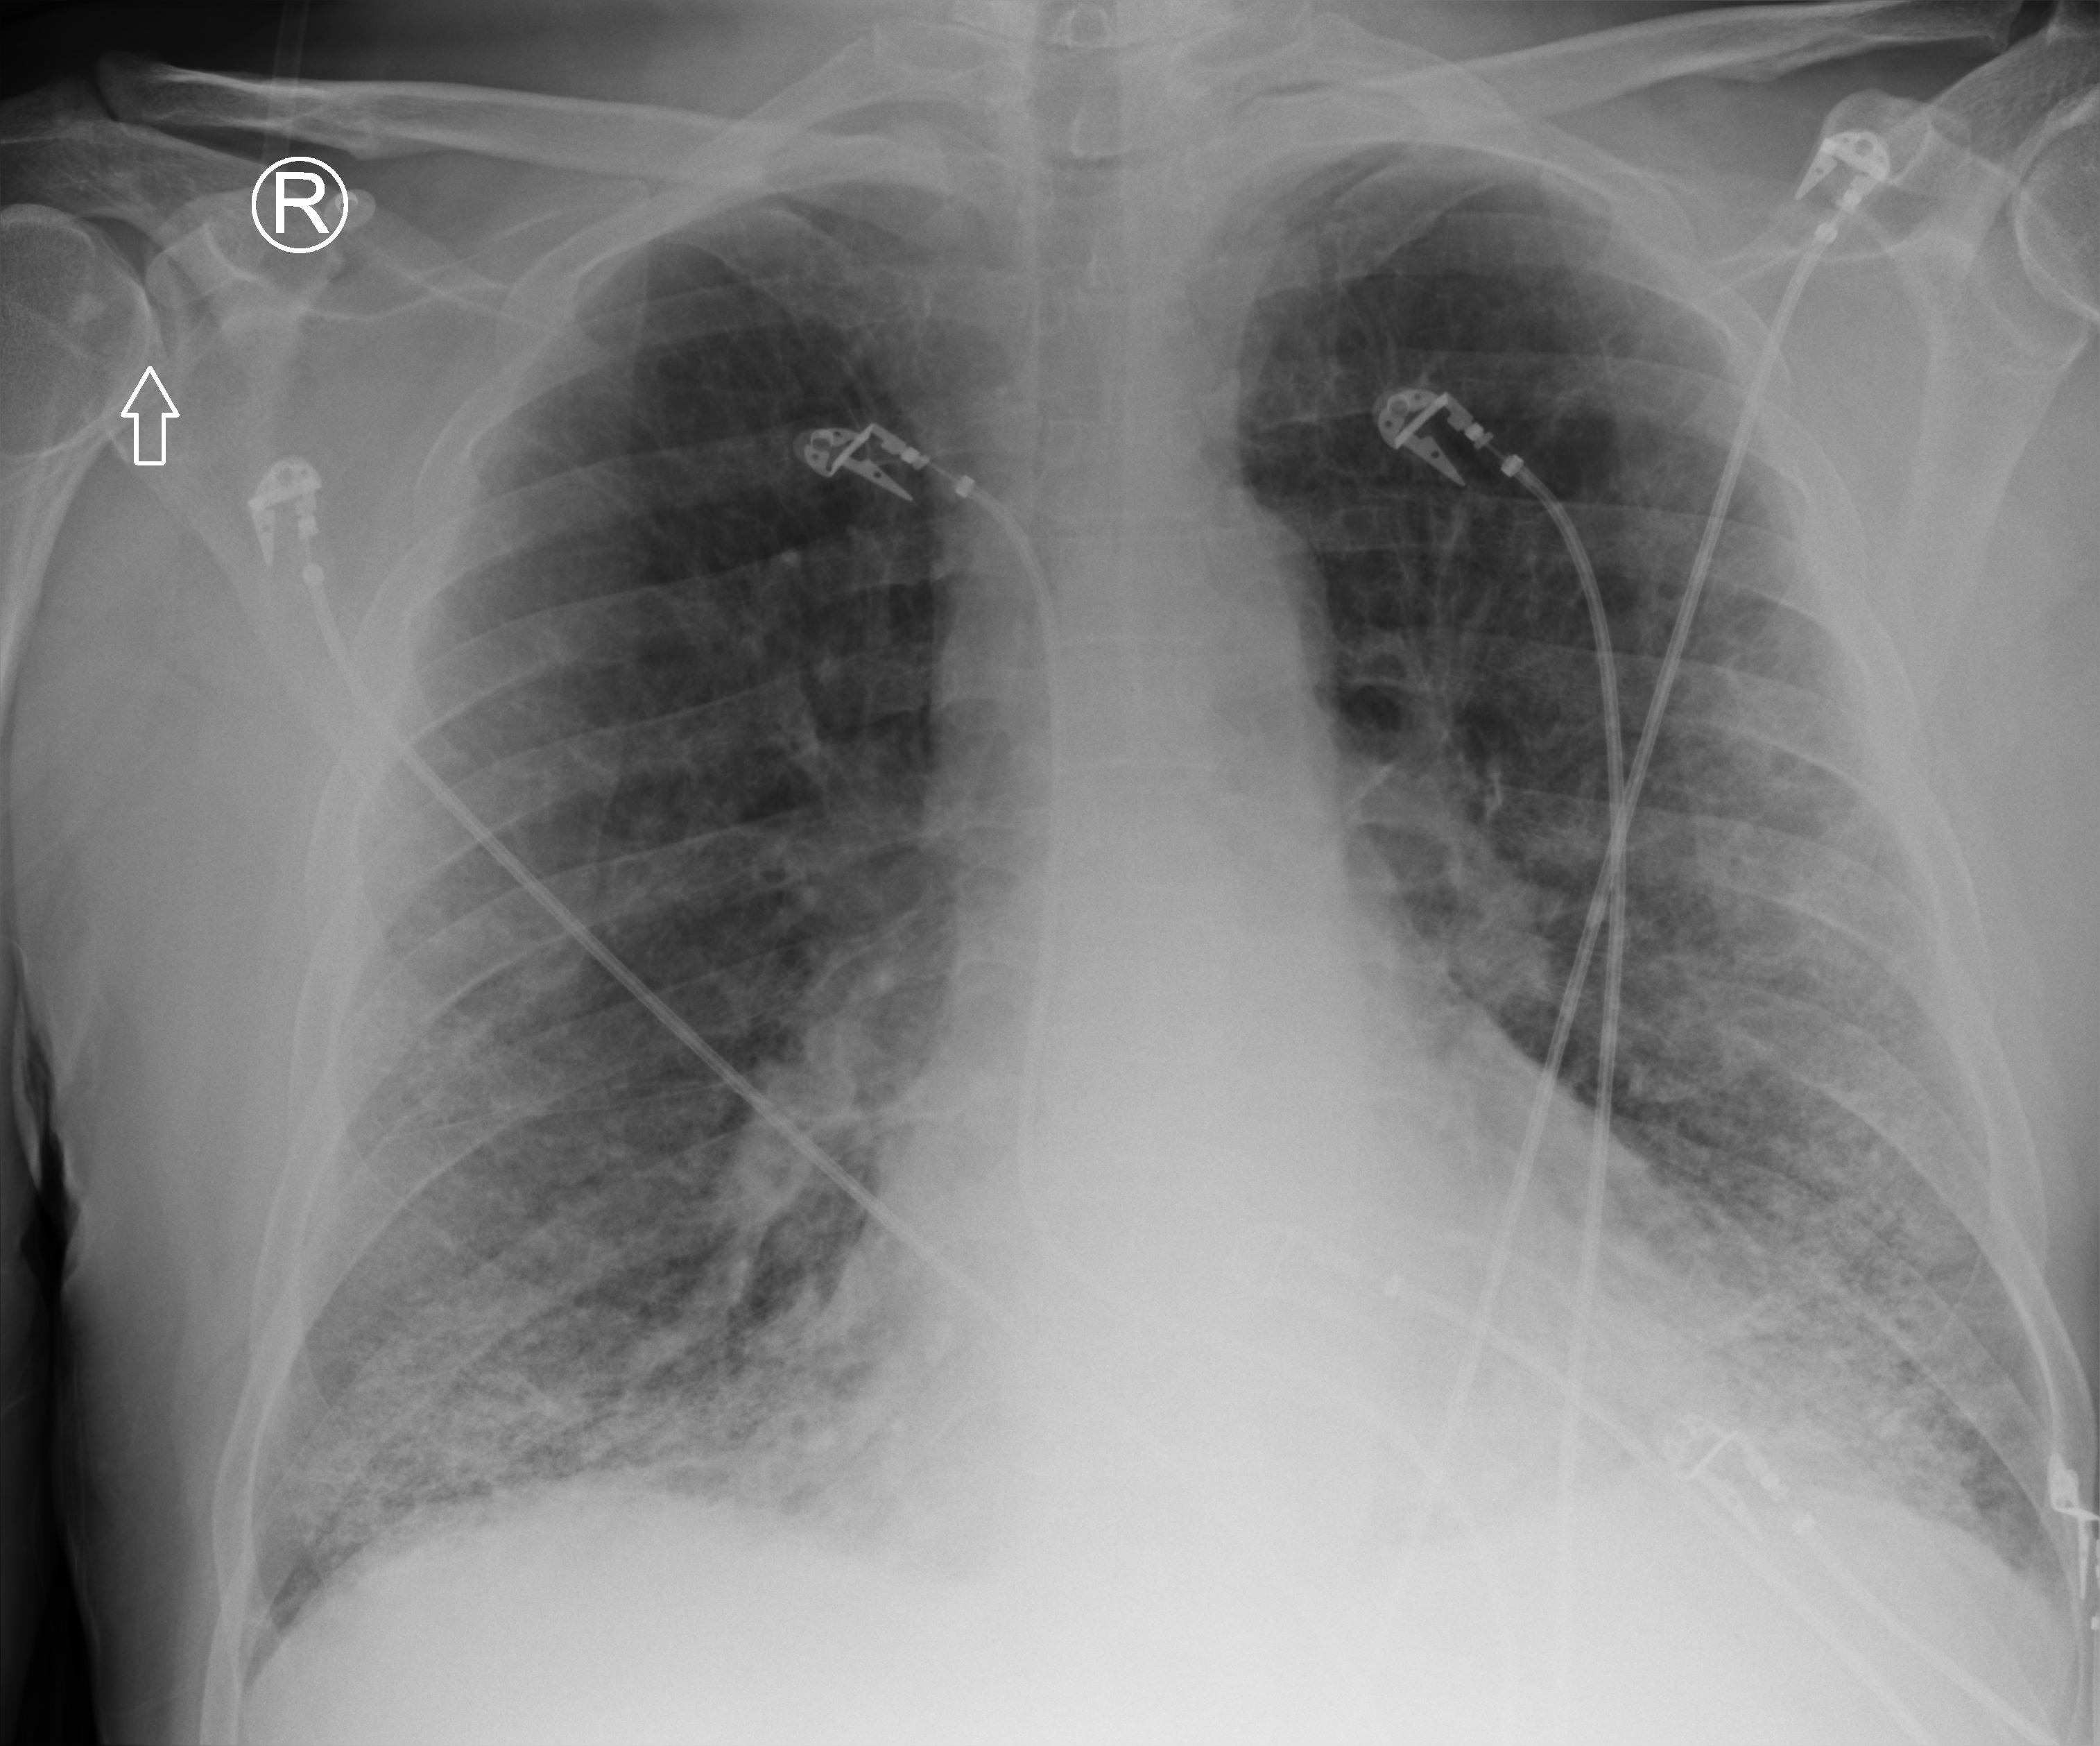
Portable chest radiograph. Patient hospitalised with COVID-19, aged 18–59 years.
From the hospital-stay record, not from the radiograph (when in the stay this image was taken is not recorded):
- other chronic lung disease (admission record): yes
- mechanically ventilated during this hospital stay: no
- admitted to intensive care during this hospital stay: yes